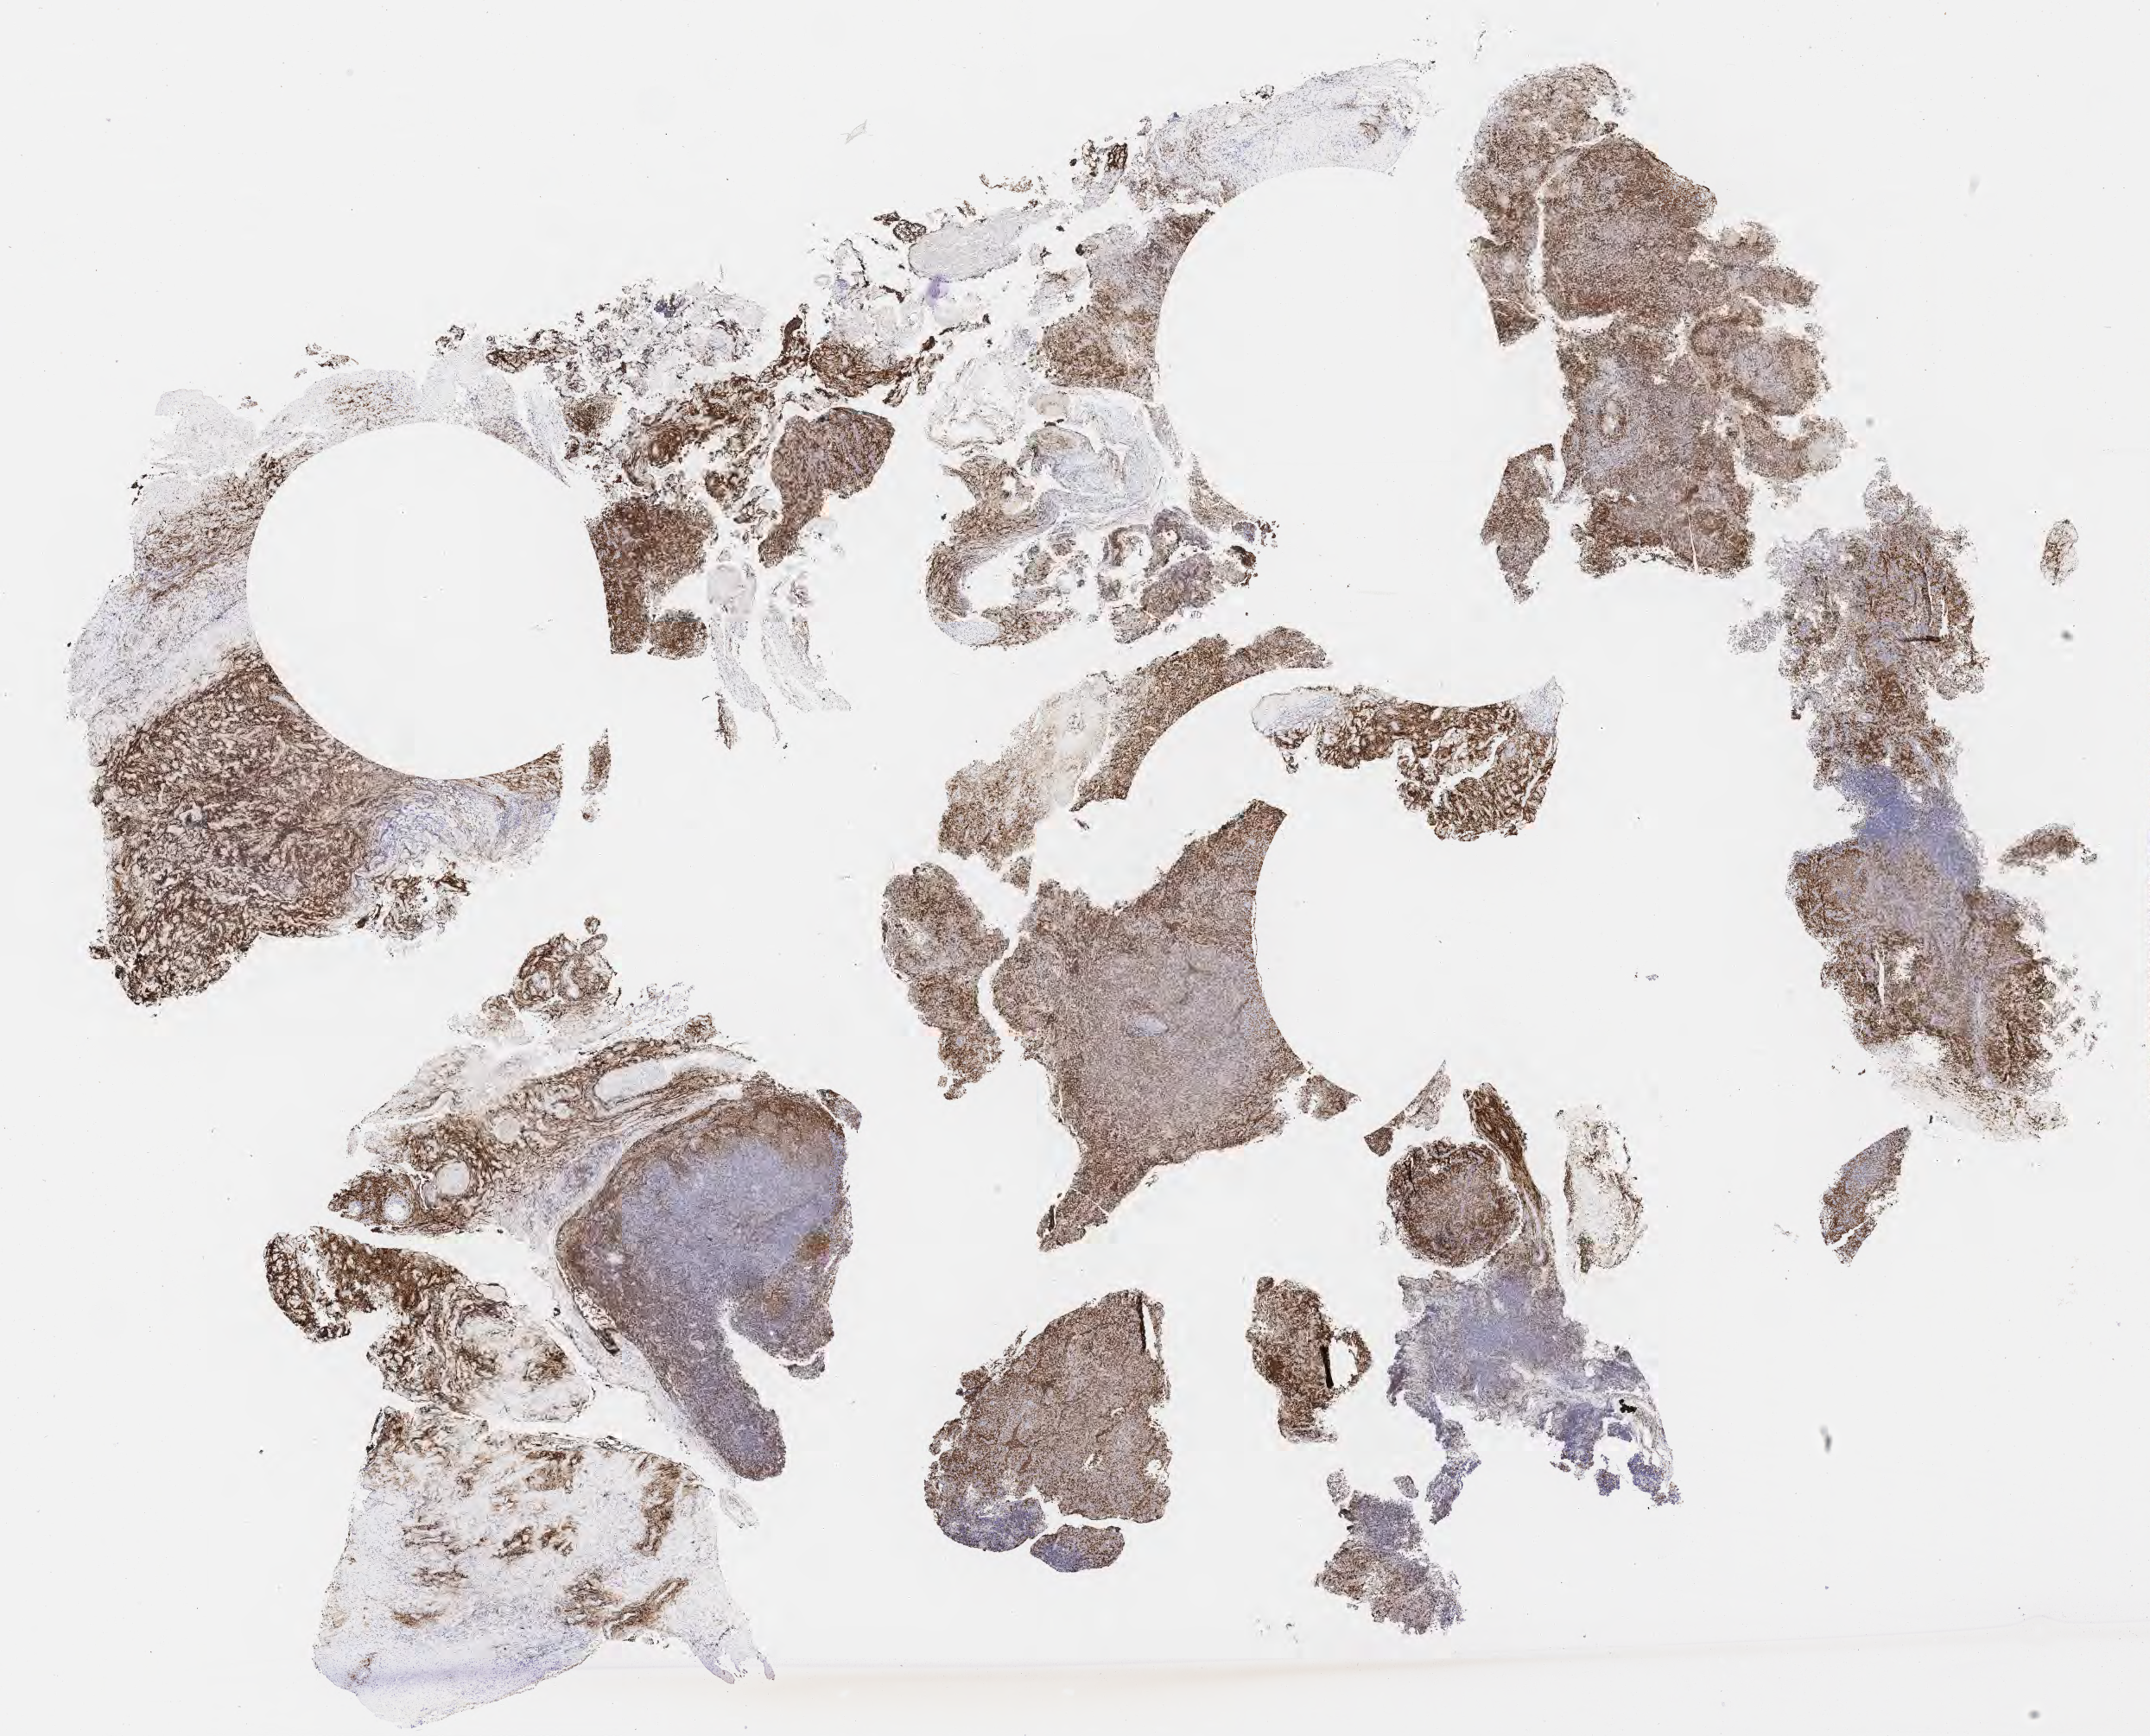
Whole-slide image, immunohistochemical stain for CD79a, shown as a low-resolution overview of the whole scanned area (about 20.1 x 16.3 mm), tumor tissue, site: lymph node. Patient male; aged 29.
- diagnosis: Diffuse large B-cell lymphoma, NOS